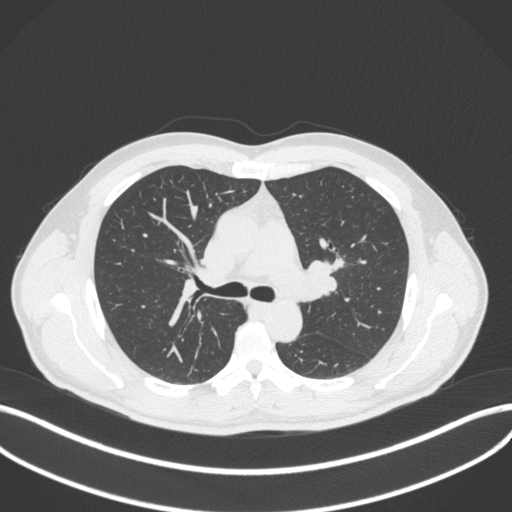
Chest CT, one axial slice; slice 272 of 383 in the series (ordered by position); reconstruction kernel B31f; lung window (W 1500 / L -600 HU); 512 × 512 image matrix, field of view 400 × 400 mm. Male patient, age 50 years. Case-level facts recorded for this patient, not image findings: clinical TNM (as recorded): T1c N1 M1b.
Outlined on this slice (bounding box drawn by a radiologist):
- lung tumour (recorded histology: squamous cell carcinoma): box from (x=329, y=254) to (x=348, y=274) px